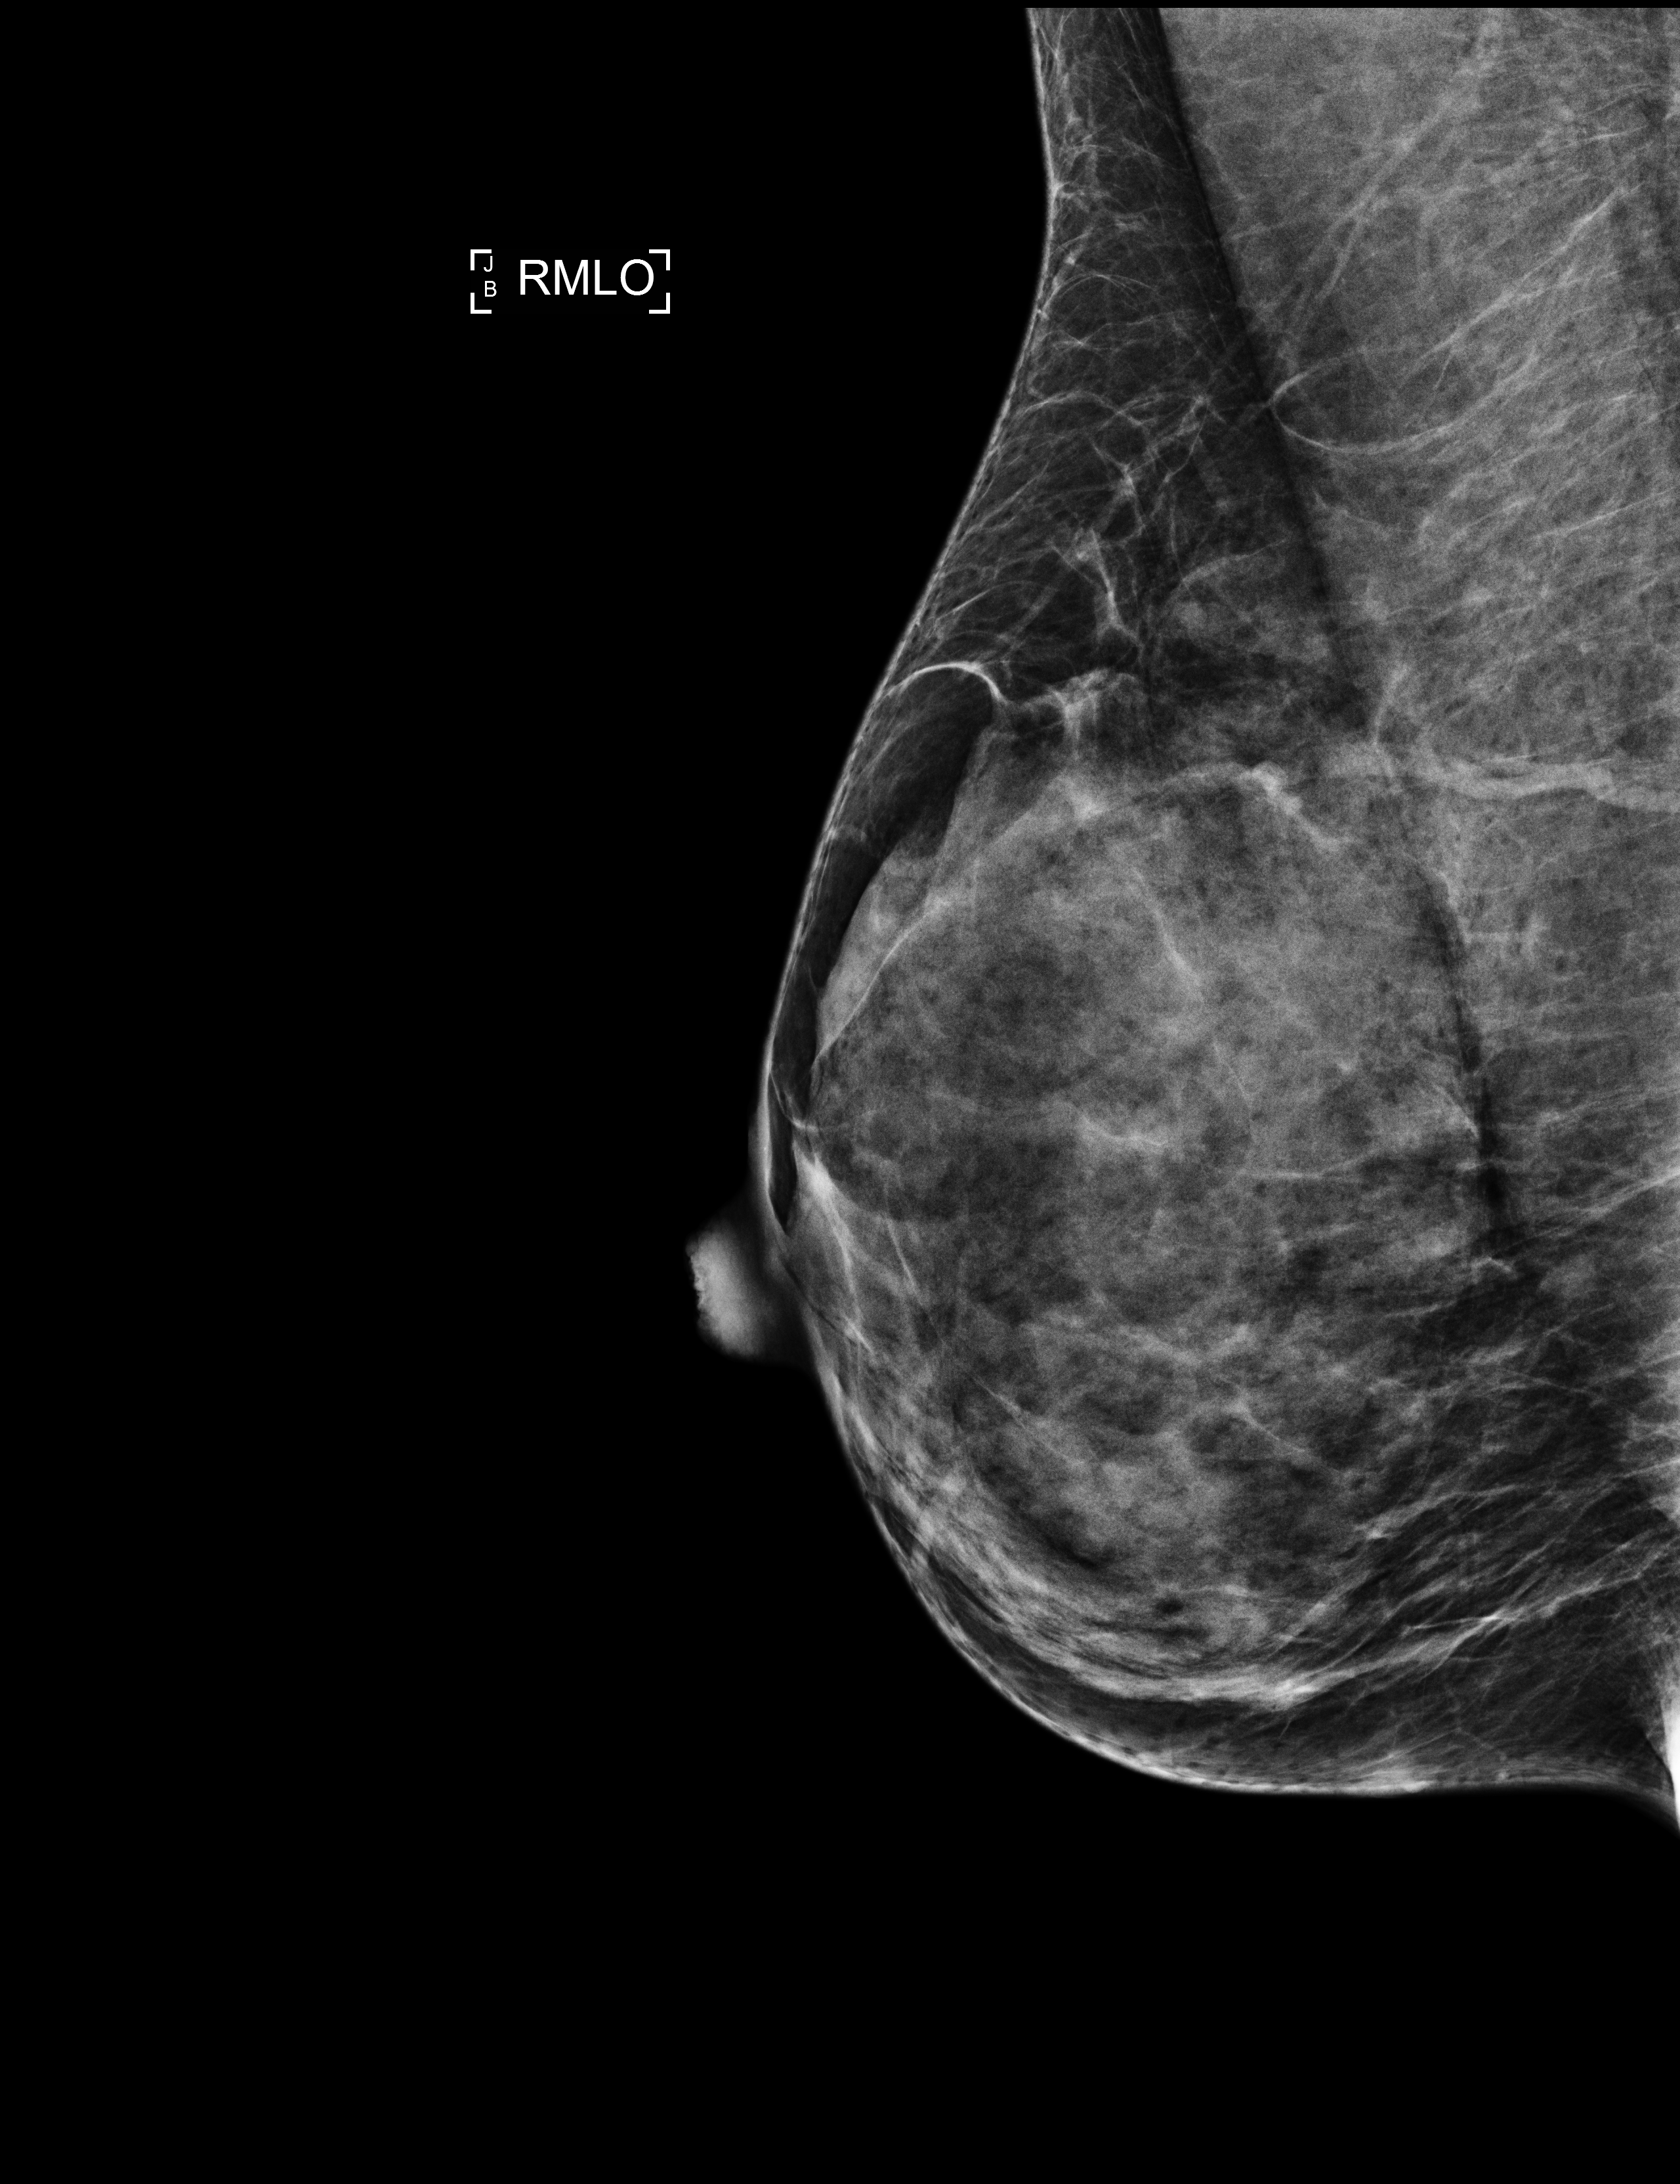
Screening examination. Patient aged 47 years (female).
Image type: full-field digital mammogram. Breast: right. Projection: medio-lateral oblique projection.